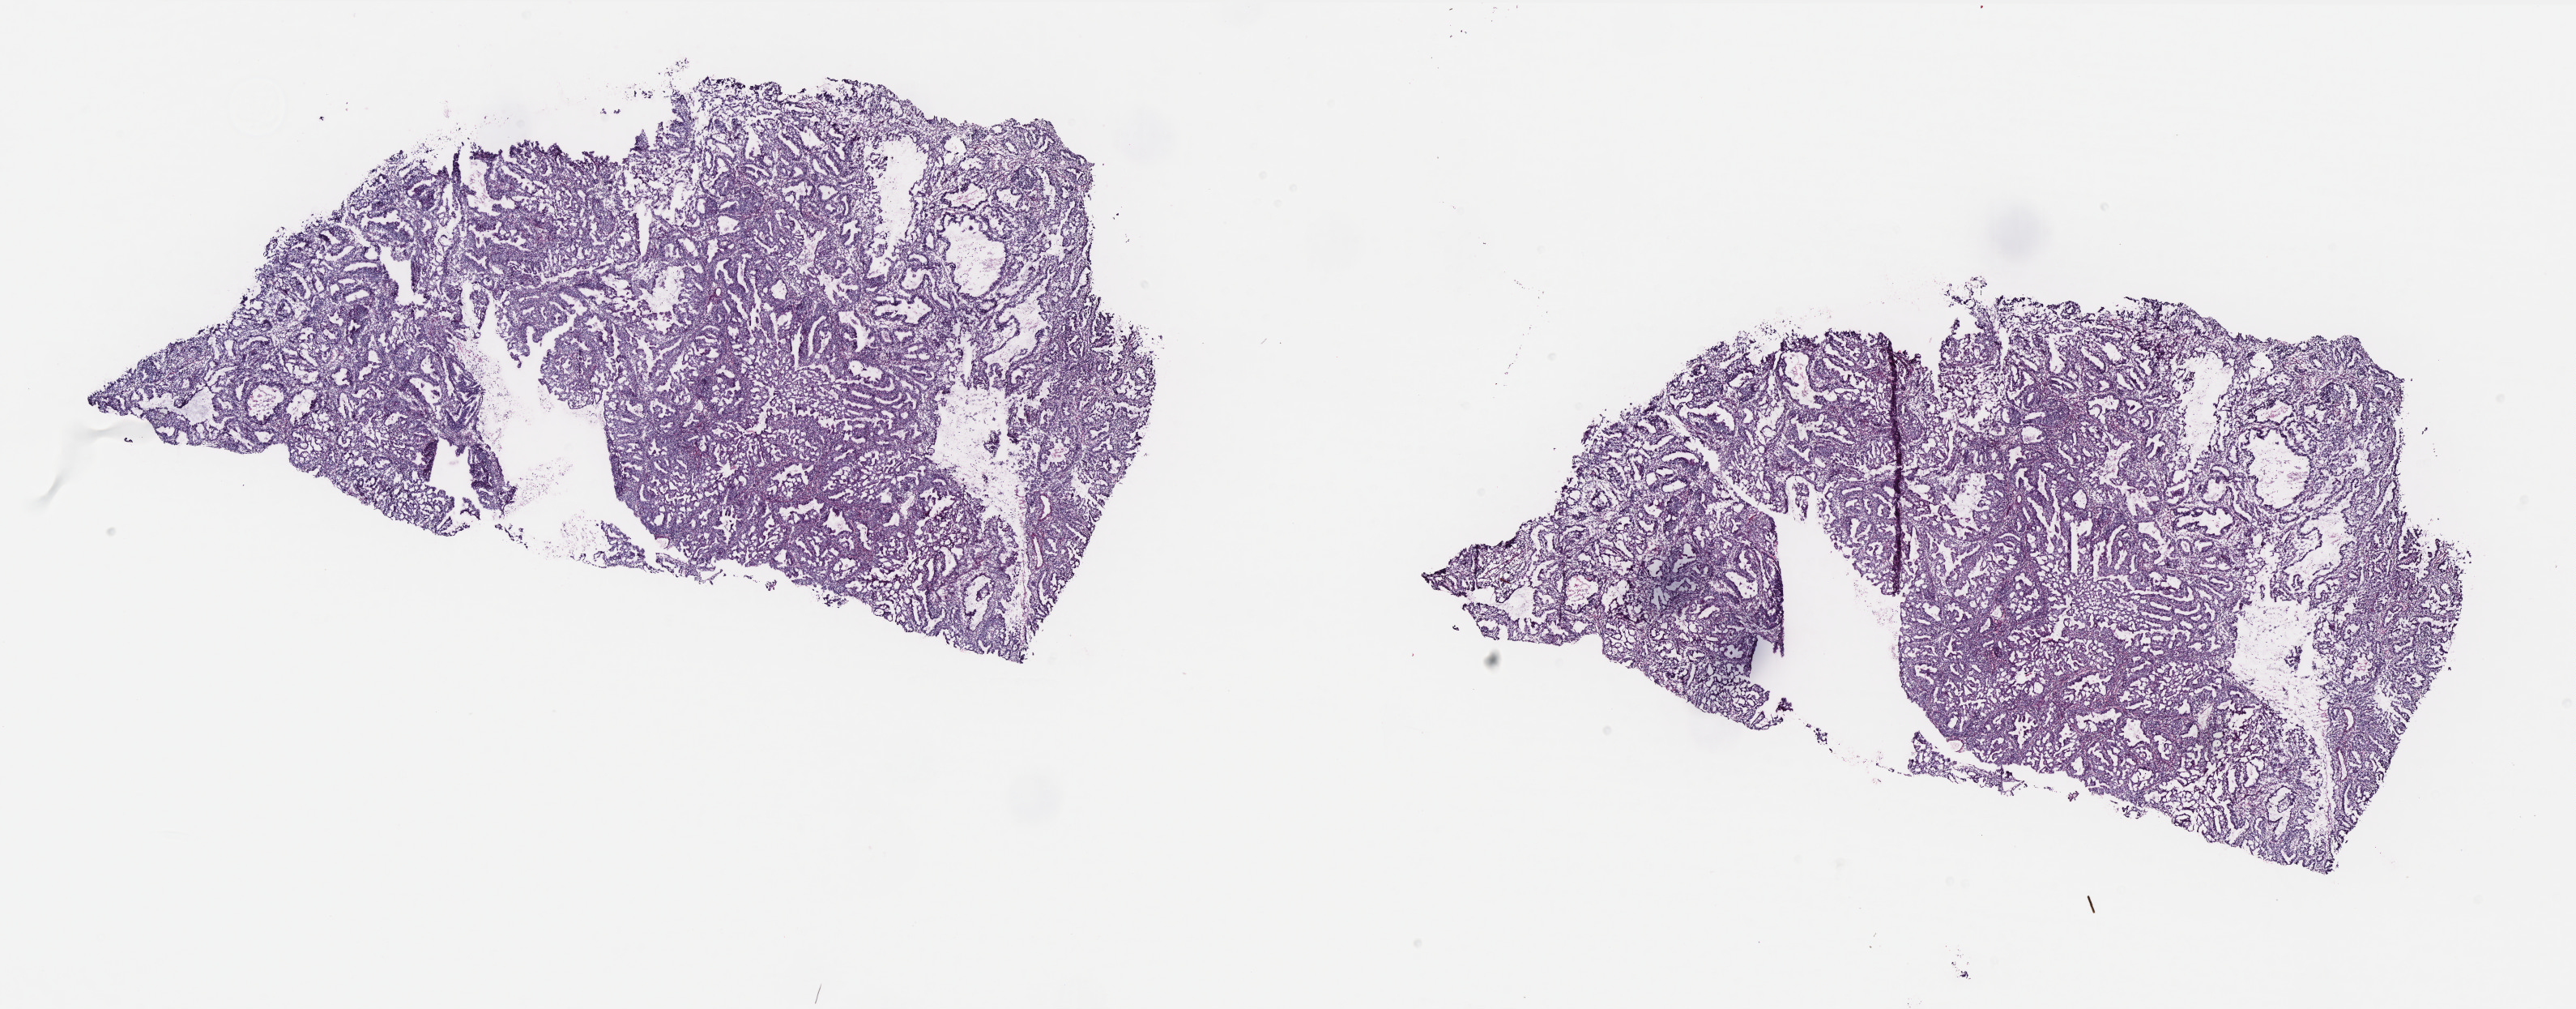
H&E-stained whole-slide image — a low-resolution overview of the entire scanned area, about 25.5 x 10.0 mm; frozen section from the bottom of the tissue portion; sample: primary tumour, uterus. Female patient; age at initial diagnosis 74 years. Slide review estimates, as recorded: tumour cells 100%, tumour nuclei 80%.
Pathologic diagnosis: Endometrioid adenocarcinoma, NOS.